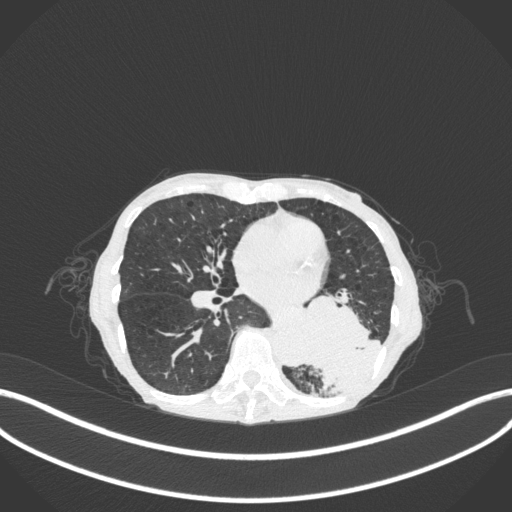
Chest CT, one axial slice. Position 123 of 347 along the scan axis. Reconstruction kernel B31f. 120 kVp. Lung window (W 1500 / L -600 HU). 1 mm slice thickness. 512 × 512 image matrix, field of view 400 × 400 mm. Female patient, age 70 years. From the clinical record (not read from this slice): clinical TNM (as recorded): T3 N0 M0.
Structures marked on this image (bounding box drawn by a radiologist):
- lung tumour (recorded histology: small cell carcinoma): bounding box <294,287,384,393> (left, top, right, bottom; pixels)